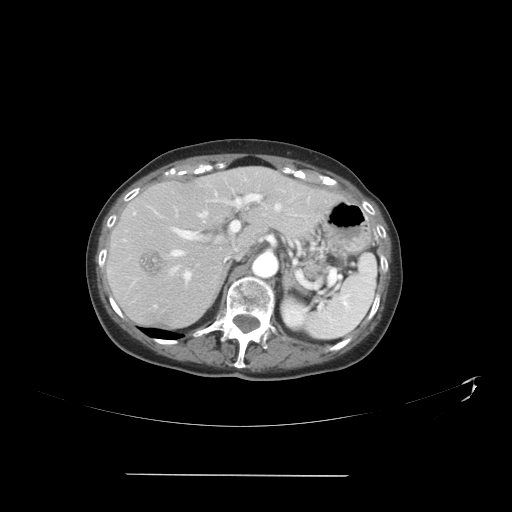
Contrast-enhanced abdominal CT, one axial slice. Position 26 of 41 along the scan axis. 120 kVp. Intravenous contrast given. Soft-tissue window (W 400 / L 40 HU). 5 mm slice thickness. 512 × 512 image matrix, field of view 431 × 431 mm. Female patient, age 74 years. Case-level facts recorded for this patient, not image findings: diagnosis: colorectal cancer liver metastases, imaged before liver resection; multiple liver metastases: yes; largest metastasis: 3.3 cm; disease in both lobes: yes.
Outlined on this slice (manually delineated by an expert):
- hepatic veins: bounding box (x1, y1, x2, y2) in pixels: (170, 204, 280, 275)
- liver: (107, 167, 334, 330)
- planned liver remnant (the part of the liver to remain after resection): (116, 167, 304, 256)
- portal vein (with intrahepatic branches): (172, 194, 271, 280)
- liver metastasis: (316, 205, 324, 214)
- liver metastasis: (137, 249, 165, 278)